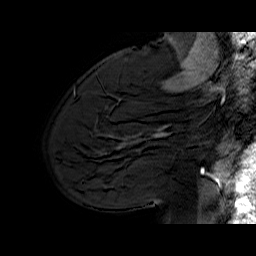
Breast MRI (dynamic contrast-enhanced), one sagittal slice; dynamic contrast-enhanced series, time point 2 of 6 at this slice position (early post-contrast); 1.5 T; TE 6.5 ms, TR 33 ms; 4 mm slice thickness; 256 × 256 image matrix. Female patient. From the clinical record (not read from this slice): setting: breast cancer imaged before/during neoadjuvant chemotherapy; receptor status: HER2-positive.
Structures marked on this image (semi-automatically segmented with operator editing):
- analysis volume of interest (the breast-tissue region the enhancement analysis was run in; not a lesion): box from (x=113, y=112) to (x=174, y=170) px
- tumour enhancement mask (voxels above the 100 % enhancement threshold inside the analysis volume of interest): (x=117, y=125)–(x=168, y=149)